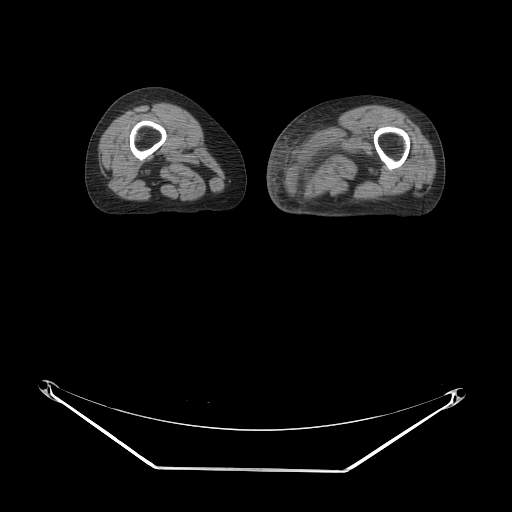
CT of an extremity soft-tissue mass (from a PET/CT study), one axial slice; slice 14 of 91 in the series (ordered by position); reconstruction kernel STANDARD; soft-tissue window (W 400 / L 40 HU); 3.75 mm slice thickness; 512 × 512 image matrix, field of view 500 × 500 mm. Female patient. Case-level facts recorded for this patient, not image findings: histological type: pleomorphic leiomyosarcoma; grade: high; site of the primary tumour: left thigh.
Annotated regions visible in this slice (expert contour drawn on MRI and transferred to this co-registered scan by the dataset authors):
- gross tumour volume including surrounding oedema: bounding box (x1, y1, x2, y2) in pixels: (290, 126, 378, 195)
- gross tumour volume (mass): (292, 171, 318, 193)